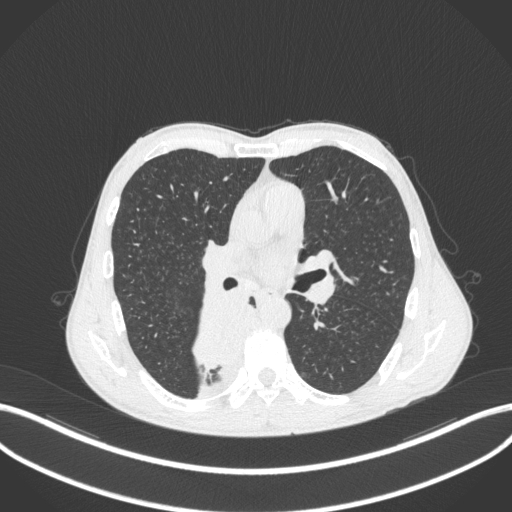
Chest CT, one axial slice. Position 211 of 371 along the scan axis. Reconstruction kernel B31f. Lung window (W 1500 / L -600 HU). 1 mm slice thickness. 512 × 512 image matrix, field of view 400 × 400 mm. Patient: male, 58 years. Case-level facts recorded for this patient, not image findings: clinical TNM (as recorded): T3 N1 M1.
Outlined on this slice (rectangle marked by the reading radiologist):
- lung tumour (recorded histology: squamous cell carcinoma): bounding box (x1, y1, x2, y2) in pixels: (190, 293, 251, 373)